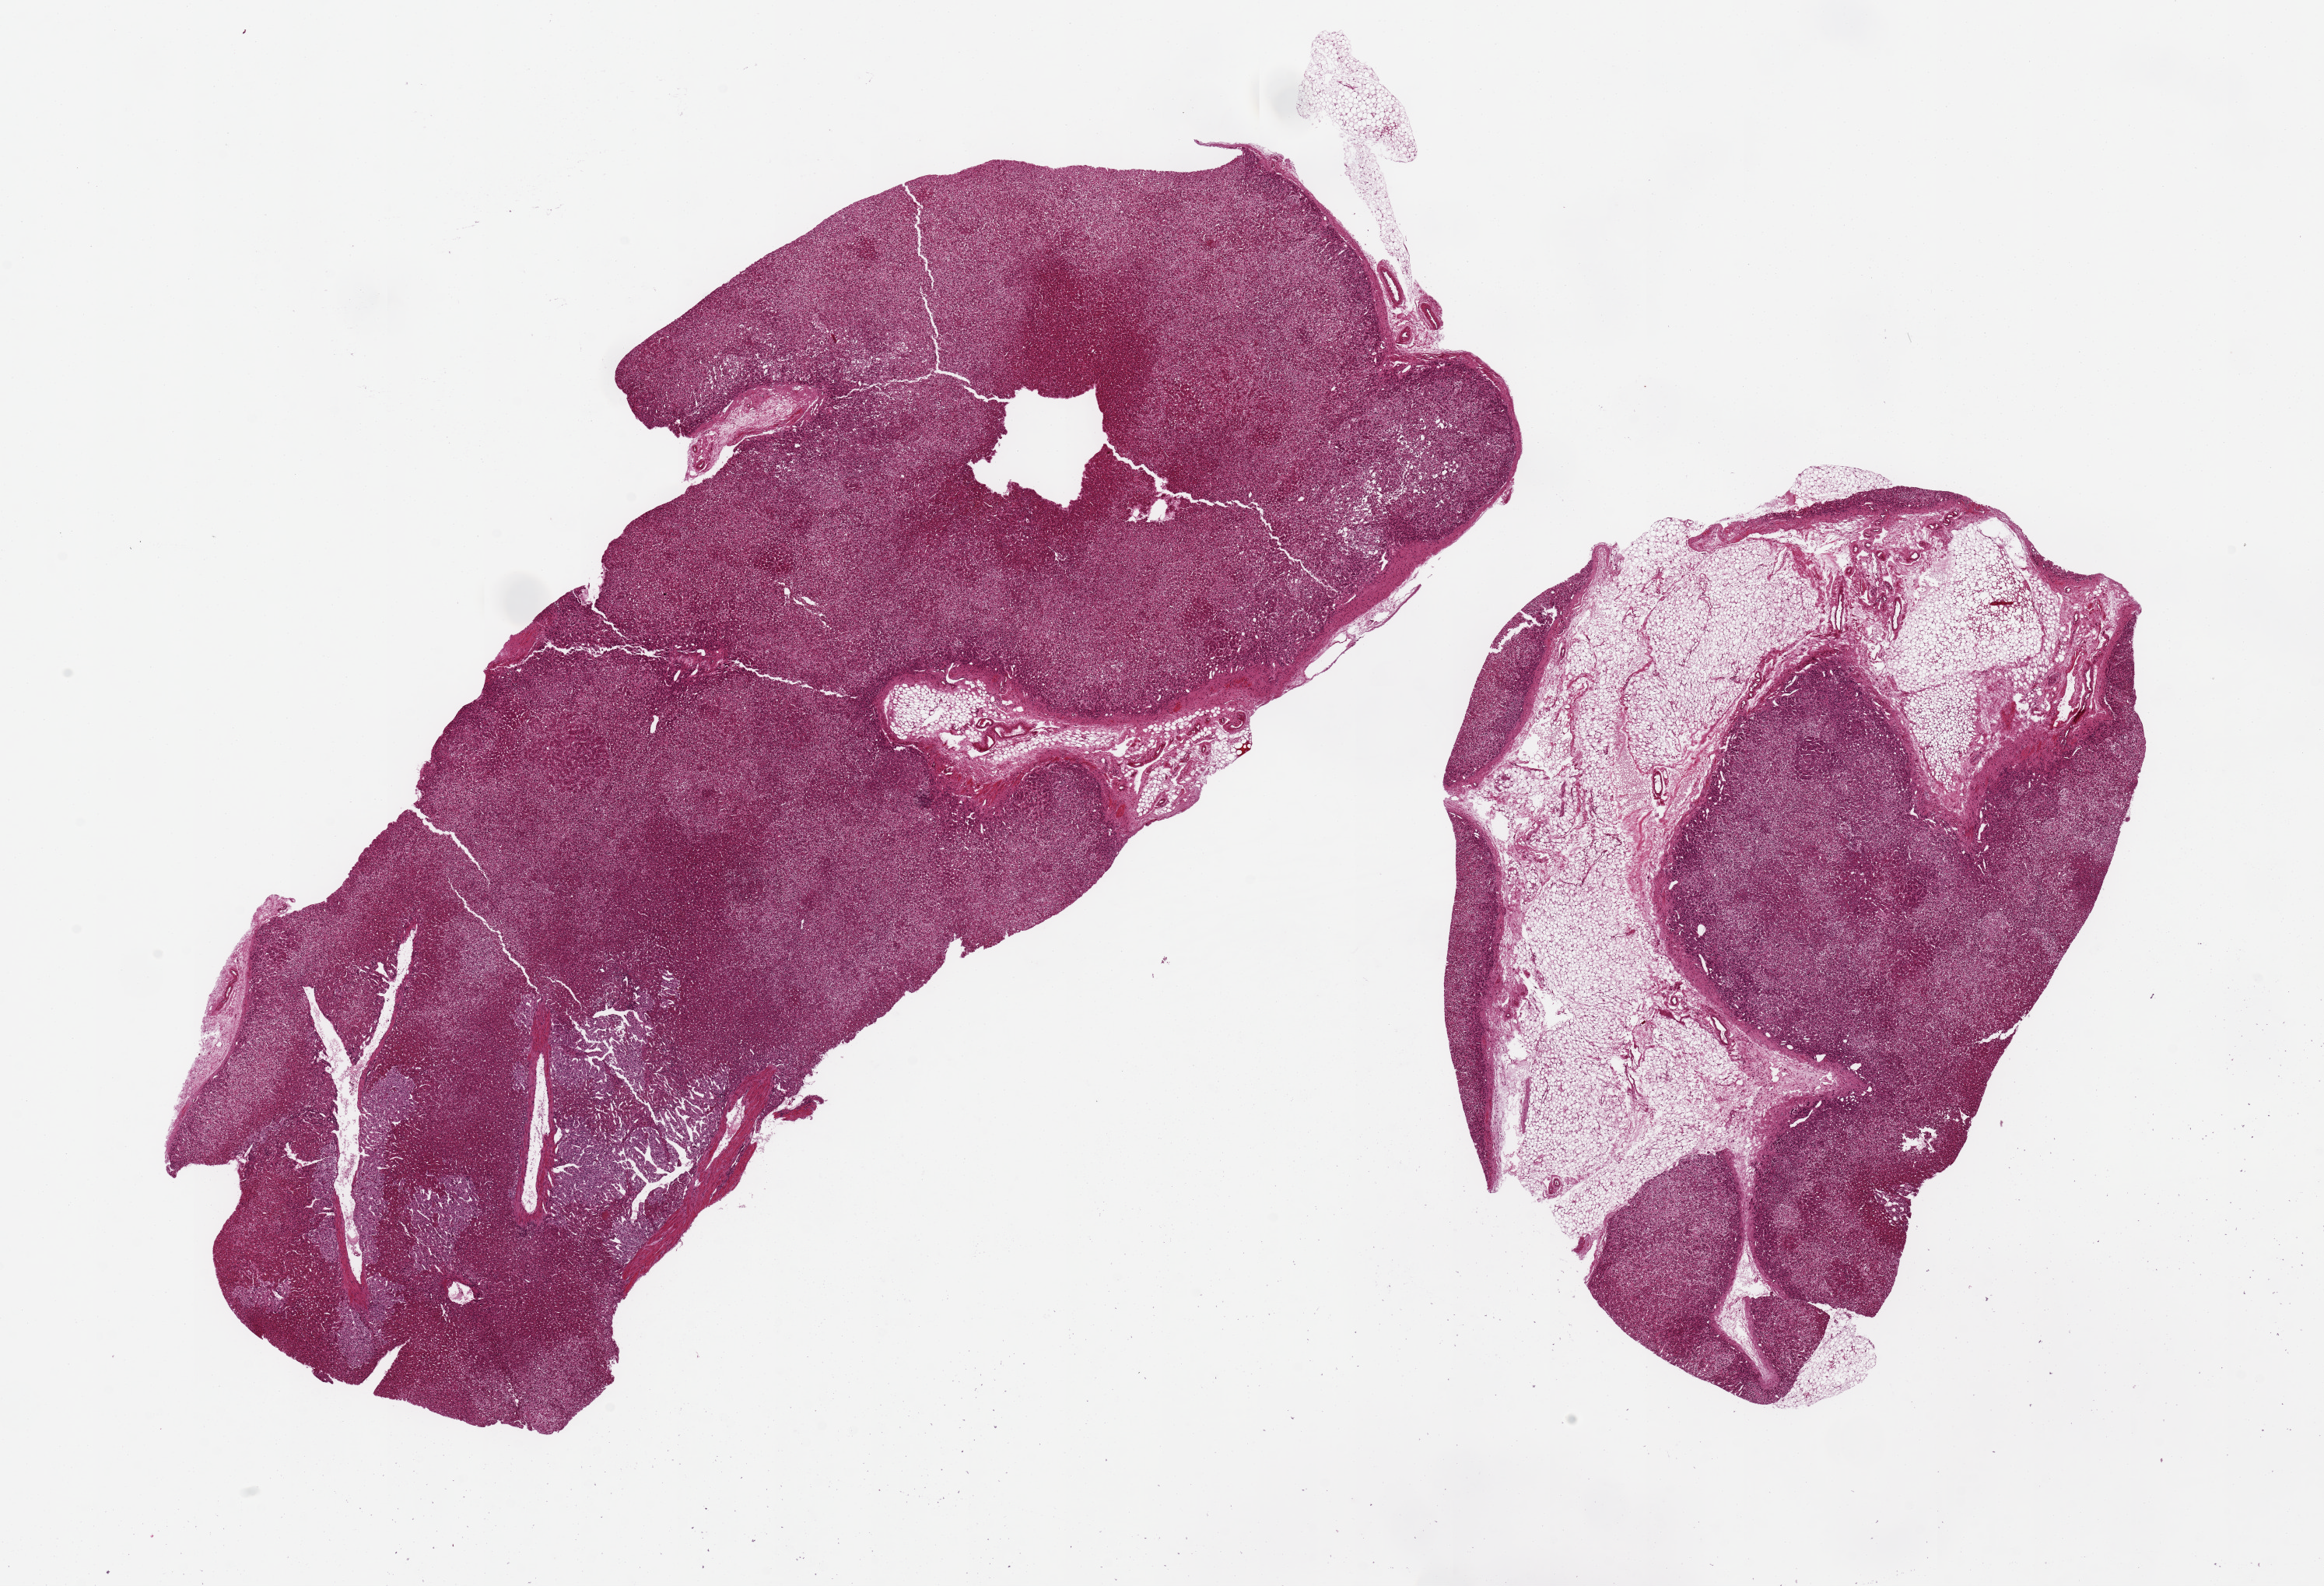
Digitized H&E-stained section, brightfield, low-resolution overview of the scanned area, about 23.6 x 16.1 mm (slide scanned at 20x); PAXgene-fixed paraffin-embedded (PFPE) section; sampled site (target tissue): adrenal gland; donor tissue sample. Donor sex: male.
Reviewer comment on this tissue sample: 2 pieces, 6x14 & 6x9 mm; largely cortex; 1 piece has.